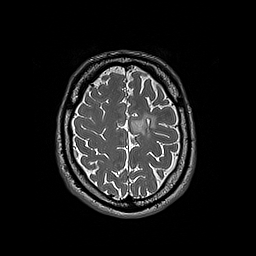
Brain MRI from a brain-tumour surgery series, one axial slice. Position 54 of 192 along the scan axis. 256 × 256 image matrix. From the clinical record (not read from this slice): histopathology: Oligodendroglioma; WHO grade: 3.
Annotated regions visible in this slice (expert manual segmentation):
- tumour: bounding box (x1, y1, x2, y2) in pixels: (131, 114, 157, 136)